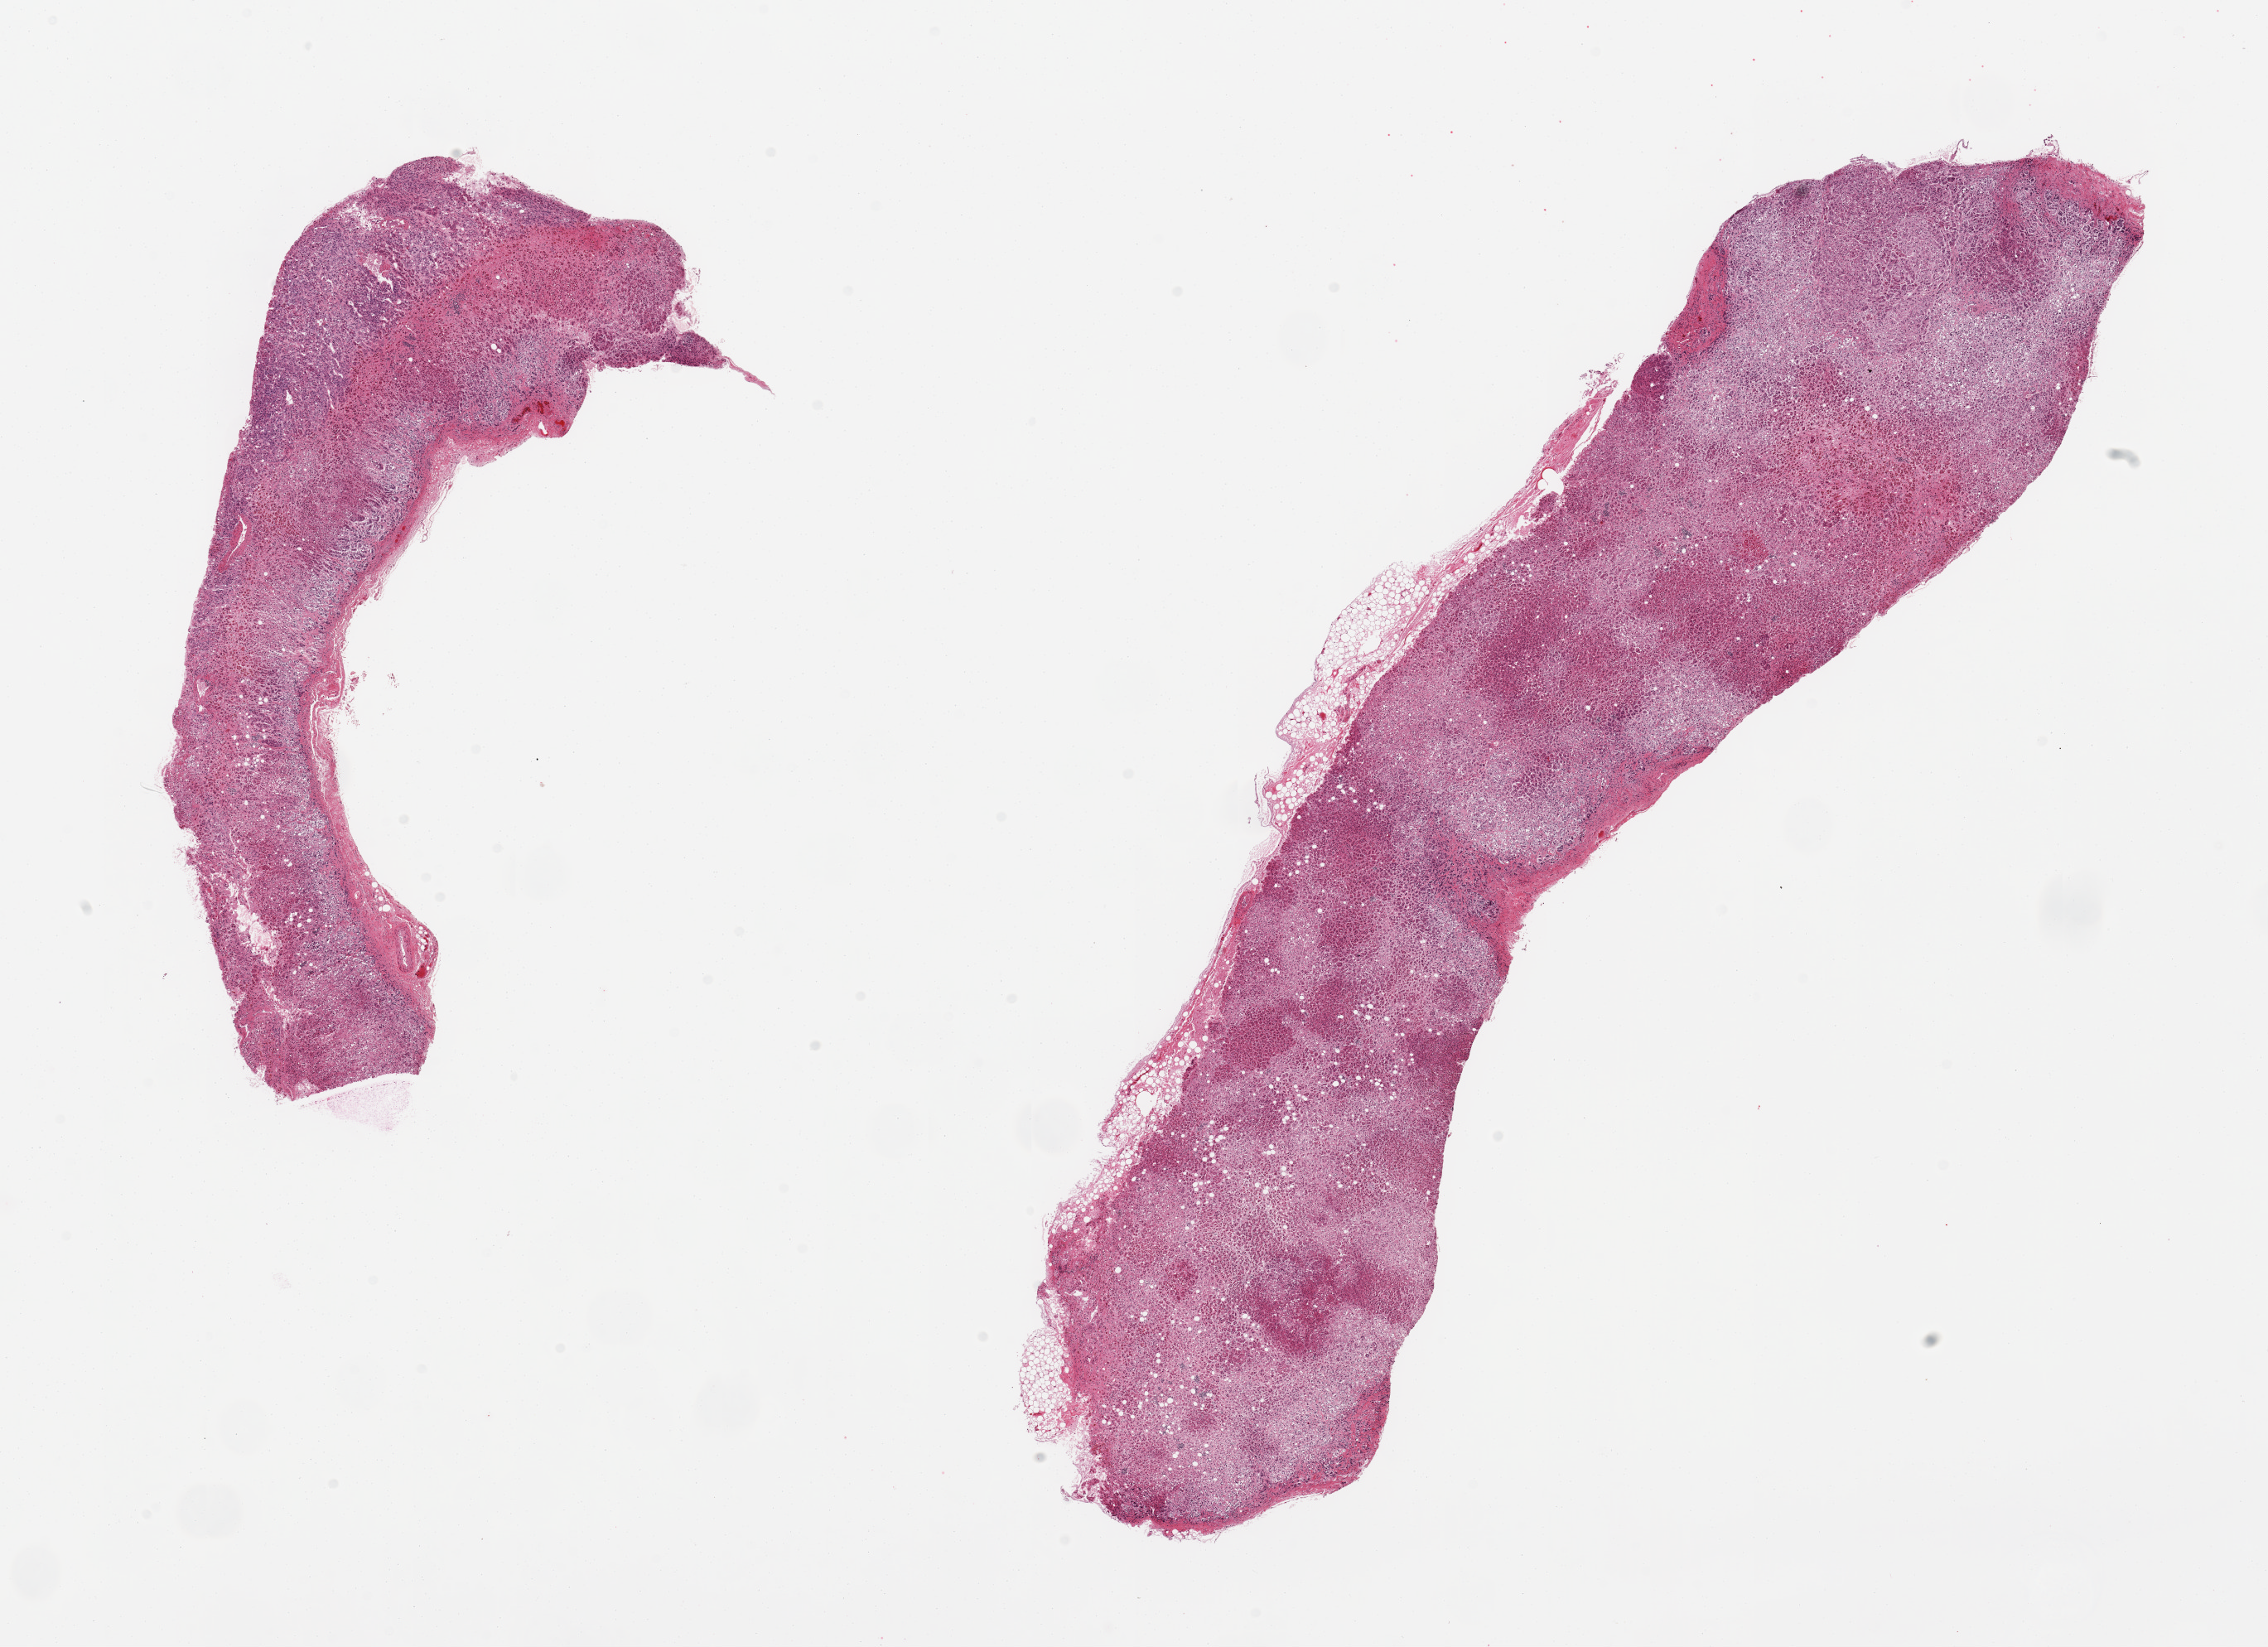
Digitized haematoxylin and eosin-stained section, whole scanned area (about 21.7 x 15.7 mm, from a 20x scan) shown as a low-resolution overview; PAXgene-fixed paraffin-embedded (PFPE) section; section of adrenal gland (target tissue); tissue donor sample. Donor sex: female.
• pathologist's review note for this sample: 2 pieces, all cortex, autolyzed